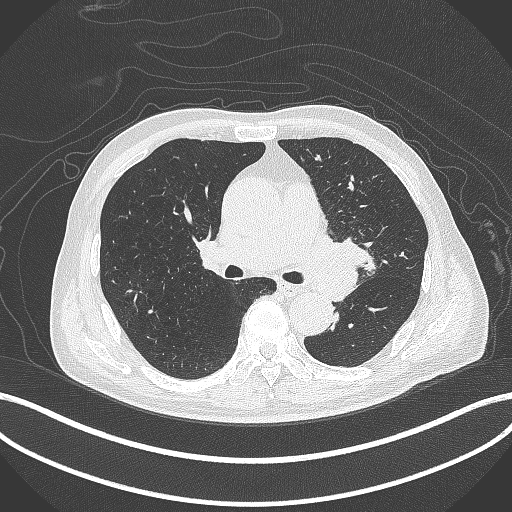
Chest CT, one axial slice; position 257 of 417 along the scan axis; lung window (W 1500 / L -600 HU); 512 × 512 image matrix, field of view 400 × 400 mm. Patient: male, 77 years. Case-level facts recorded for this patient, not image findings: clinical TNM (as recorded): T3 N1 M0.
Structures marked on this image (bounding box drawn by a radiologist):
- lung tumour (recorded histology: adenocarcinoma): bounding box [x1, y1, x2, y2] px = [311, 225, 377, 300]